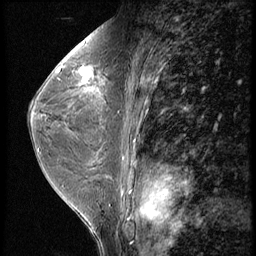
Breast MRI (dynamic contrast-enhanced), one sagittal slice; slice 30 of 56 in the series (ordered by position); 3 images stored at this slice position (order not interpretable as contrast timing); 1.5 T; TE 4.2 ms, TR 9 ms; 2.5 mm slice thickness; 256 × 256 image matrix. Patient: female, 44 years. From the clinical record (not read from this slice): setting: breast cancer imaged before/during neoadjuvant chemotherapy; receptor status: triple-negative.
Annotated regions visible in this slice (semi-automatic segmentation, software-assisted and operator-edited):
- analysis volume of interest (the breast-tissue region the enhancement analysis was run in; not a lesion): bounding box (x1, y1, x2, y2) in pixels: (71, 54, 112, 99)
- tumour enhancement mask (voxels above the 140 % enhancement threshold inside the analysis volume of interest): (77, 66, 94, 83)